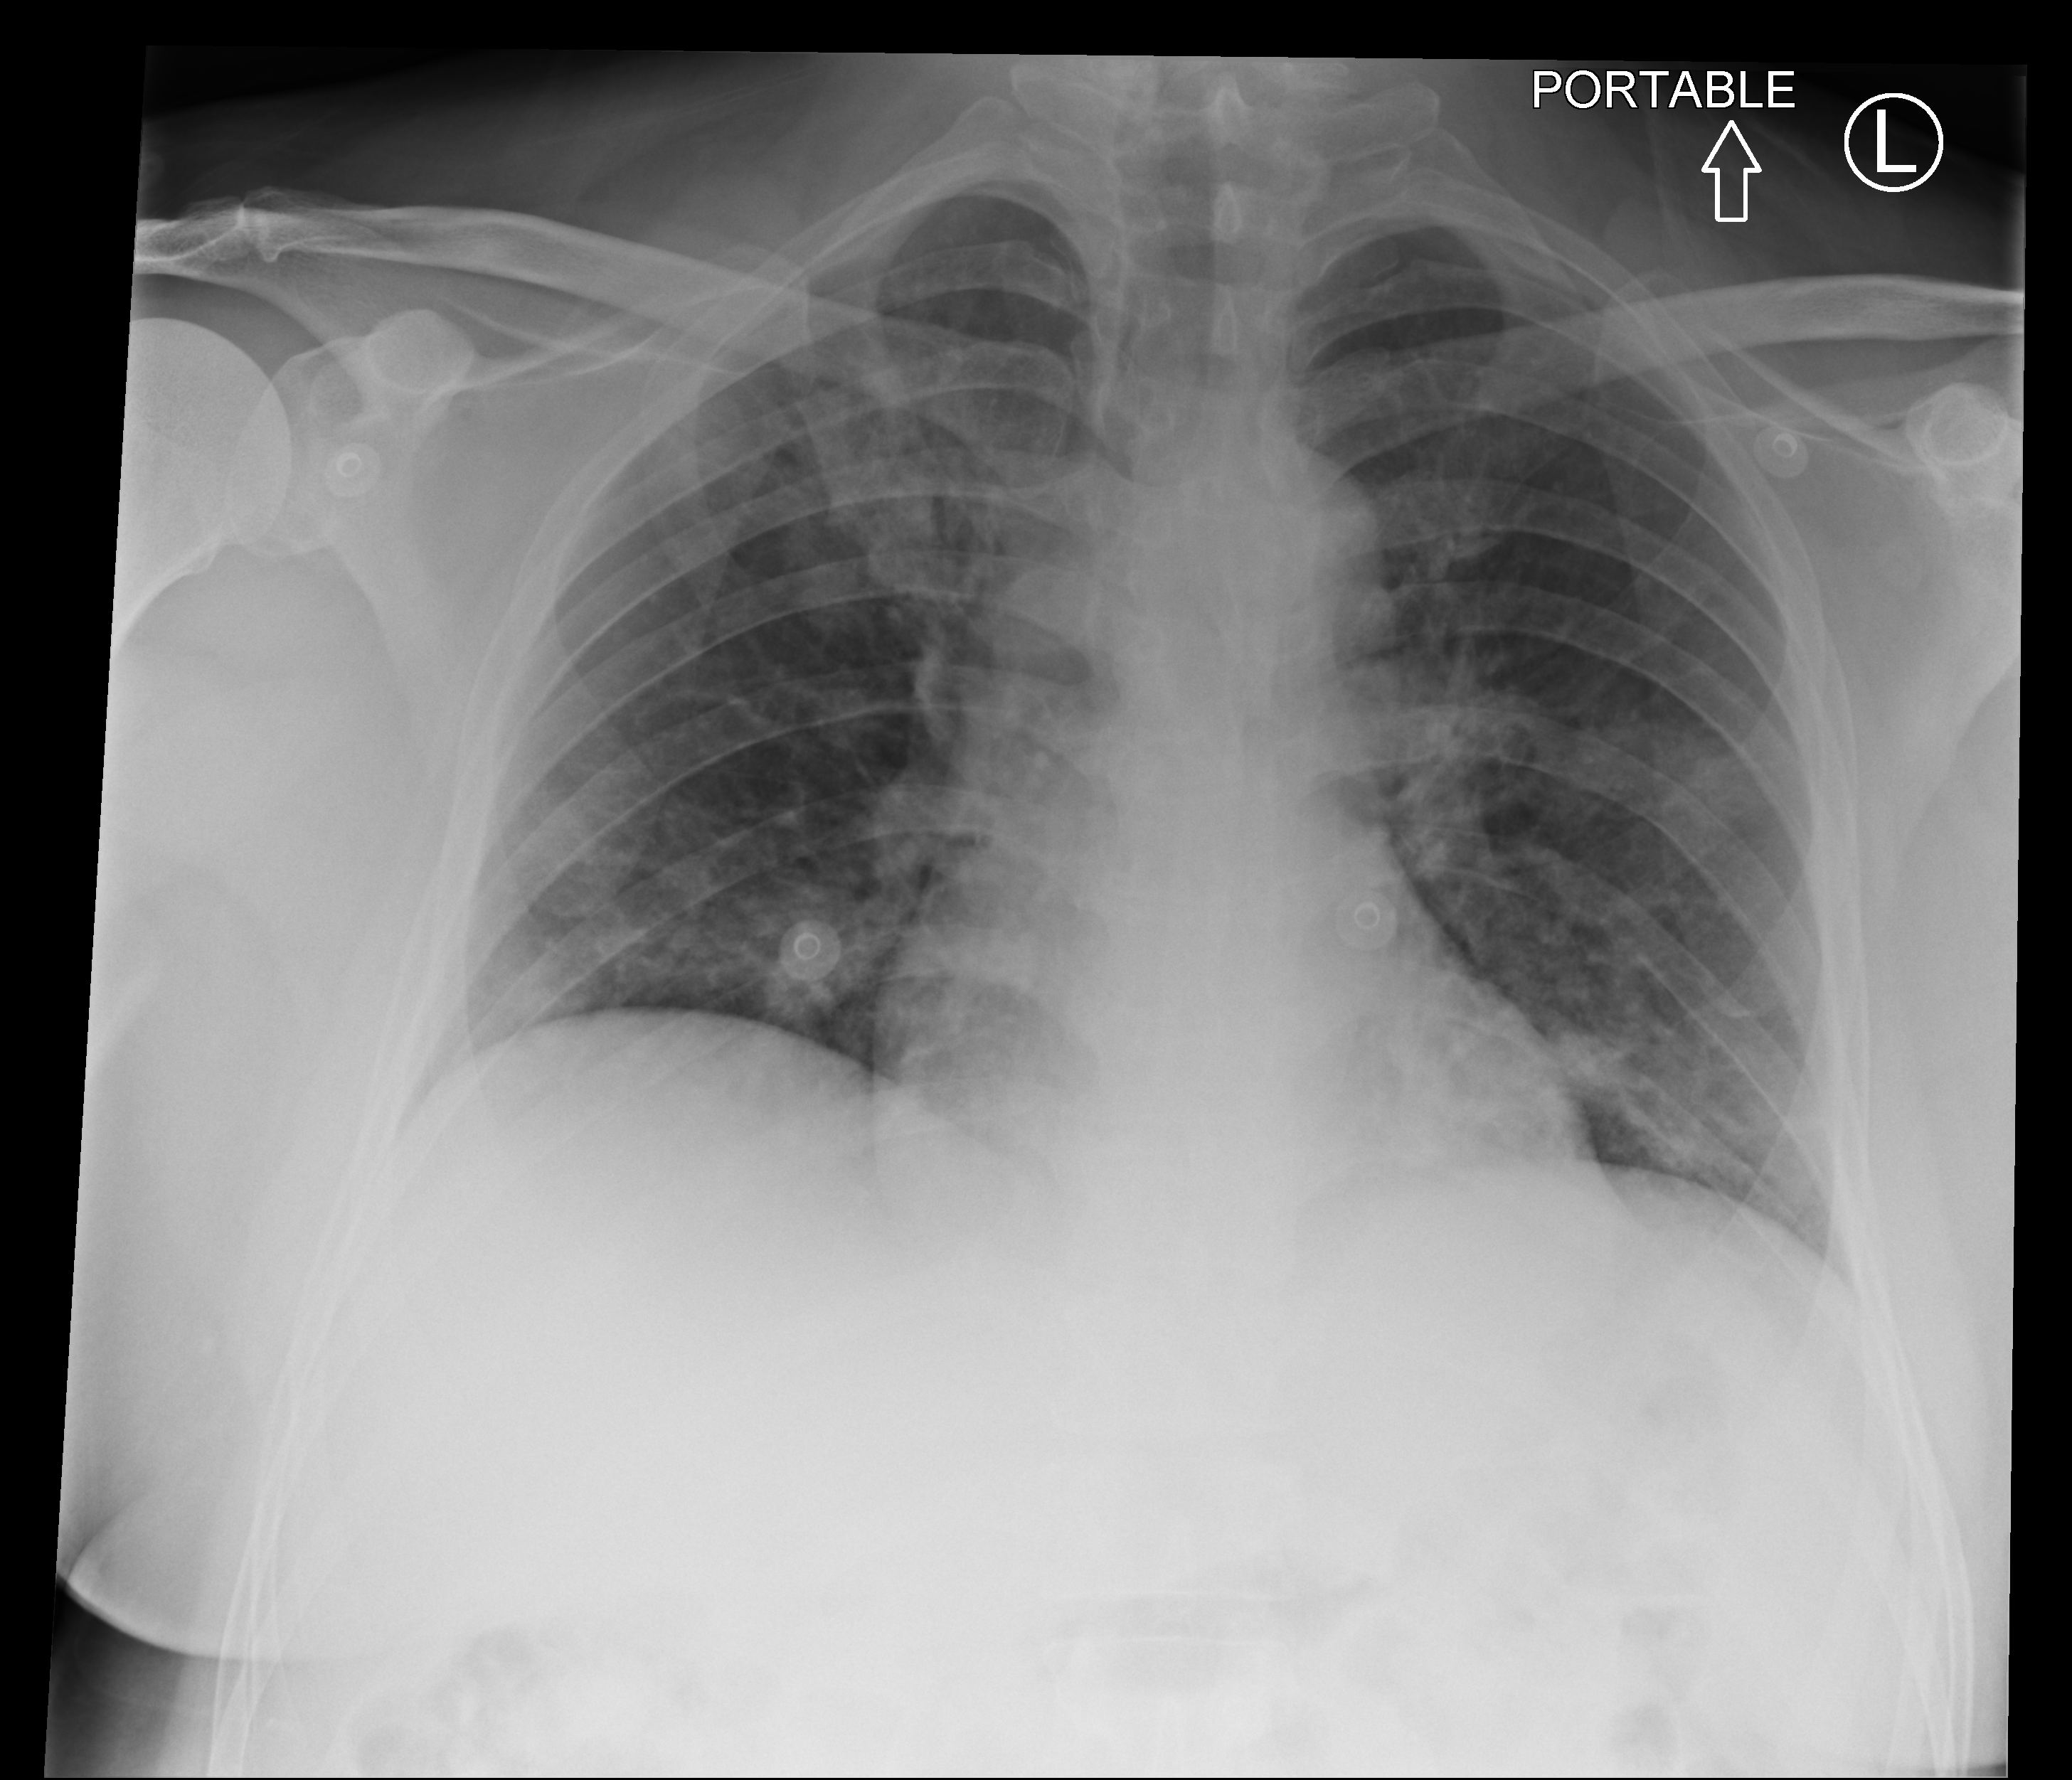
Chest X-ray (portable); anteroposterior (AP) projection. Patient hospitalised with COVID-19; male, aged 18–59 years.
From the hospital-stay record, not from the radiograph (when in the stay this image was taken is not recorded): COPD (admission record): no; hypertension (admission record): no; admitted to intensive care during this hospital stay: no.